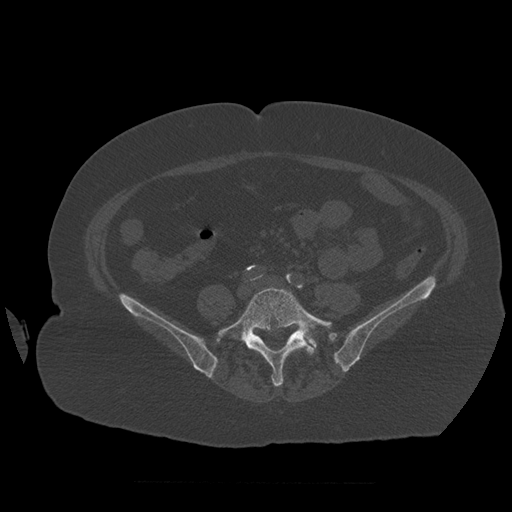
CT including the spine, one axial slice. Position 183 of 399 along the scan axis. 120 kVp. Bone window (W 1800 / L 400 HU). 1.25 mm slice thickness. 512 × 512 image matrix. Patient age 81 years. From the clinical record (not read from this slice): primary cancer: renal; vertebrae with lytic lesions (as recorded): L1.
Structures marked on this image (semi-automatically segmented with operator editing):
- L5 vertebra: bounding box [x1, y1, x2, y2] px = [218, 287, 333, 387]